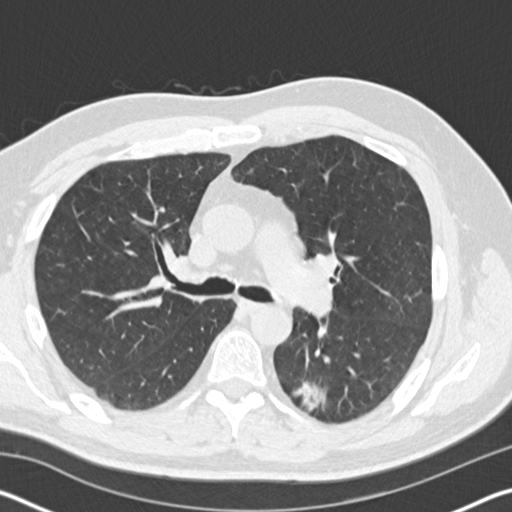
Low-dose screening chest CT, axial slice. First (baseline) screen. Lung window (W 1500 / L -600 HU). Male, age 60 years at enrolment. Current smoker at enrolment.
Expert-annotated lung lesion, bounding box [x1, y1, x2, y2] px = [276, 367, 357, 425]. The screening reader recorded 3 non-calcified nodules or masses ≥4 mm on this exam (left lower lobe, right lower lobe, right lower lobe); which of them this box marks is not recorded. Official screen result: positive, change unspecified: nodule(s) >= 4 mm or enlarging nodule(s), mass(es), or other non-specific abnormalities suspicious for lung cancer. Participant outcome: lung cancer diagnosed 171 days after this screen — papillary adenocarcinoma, NOS, left lower lobe, moderately differentiated (G2), stage IB (AJCC 6th edition), 35 mm at pathology.